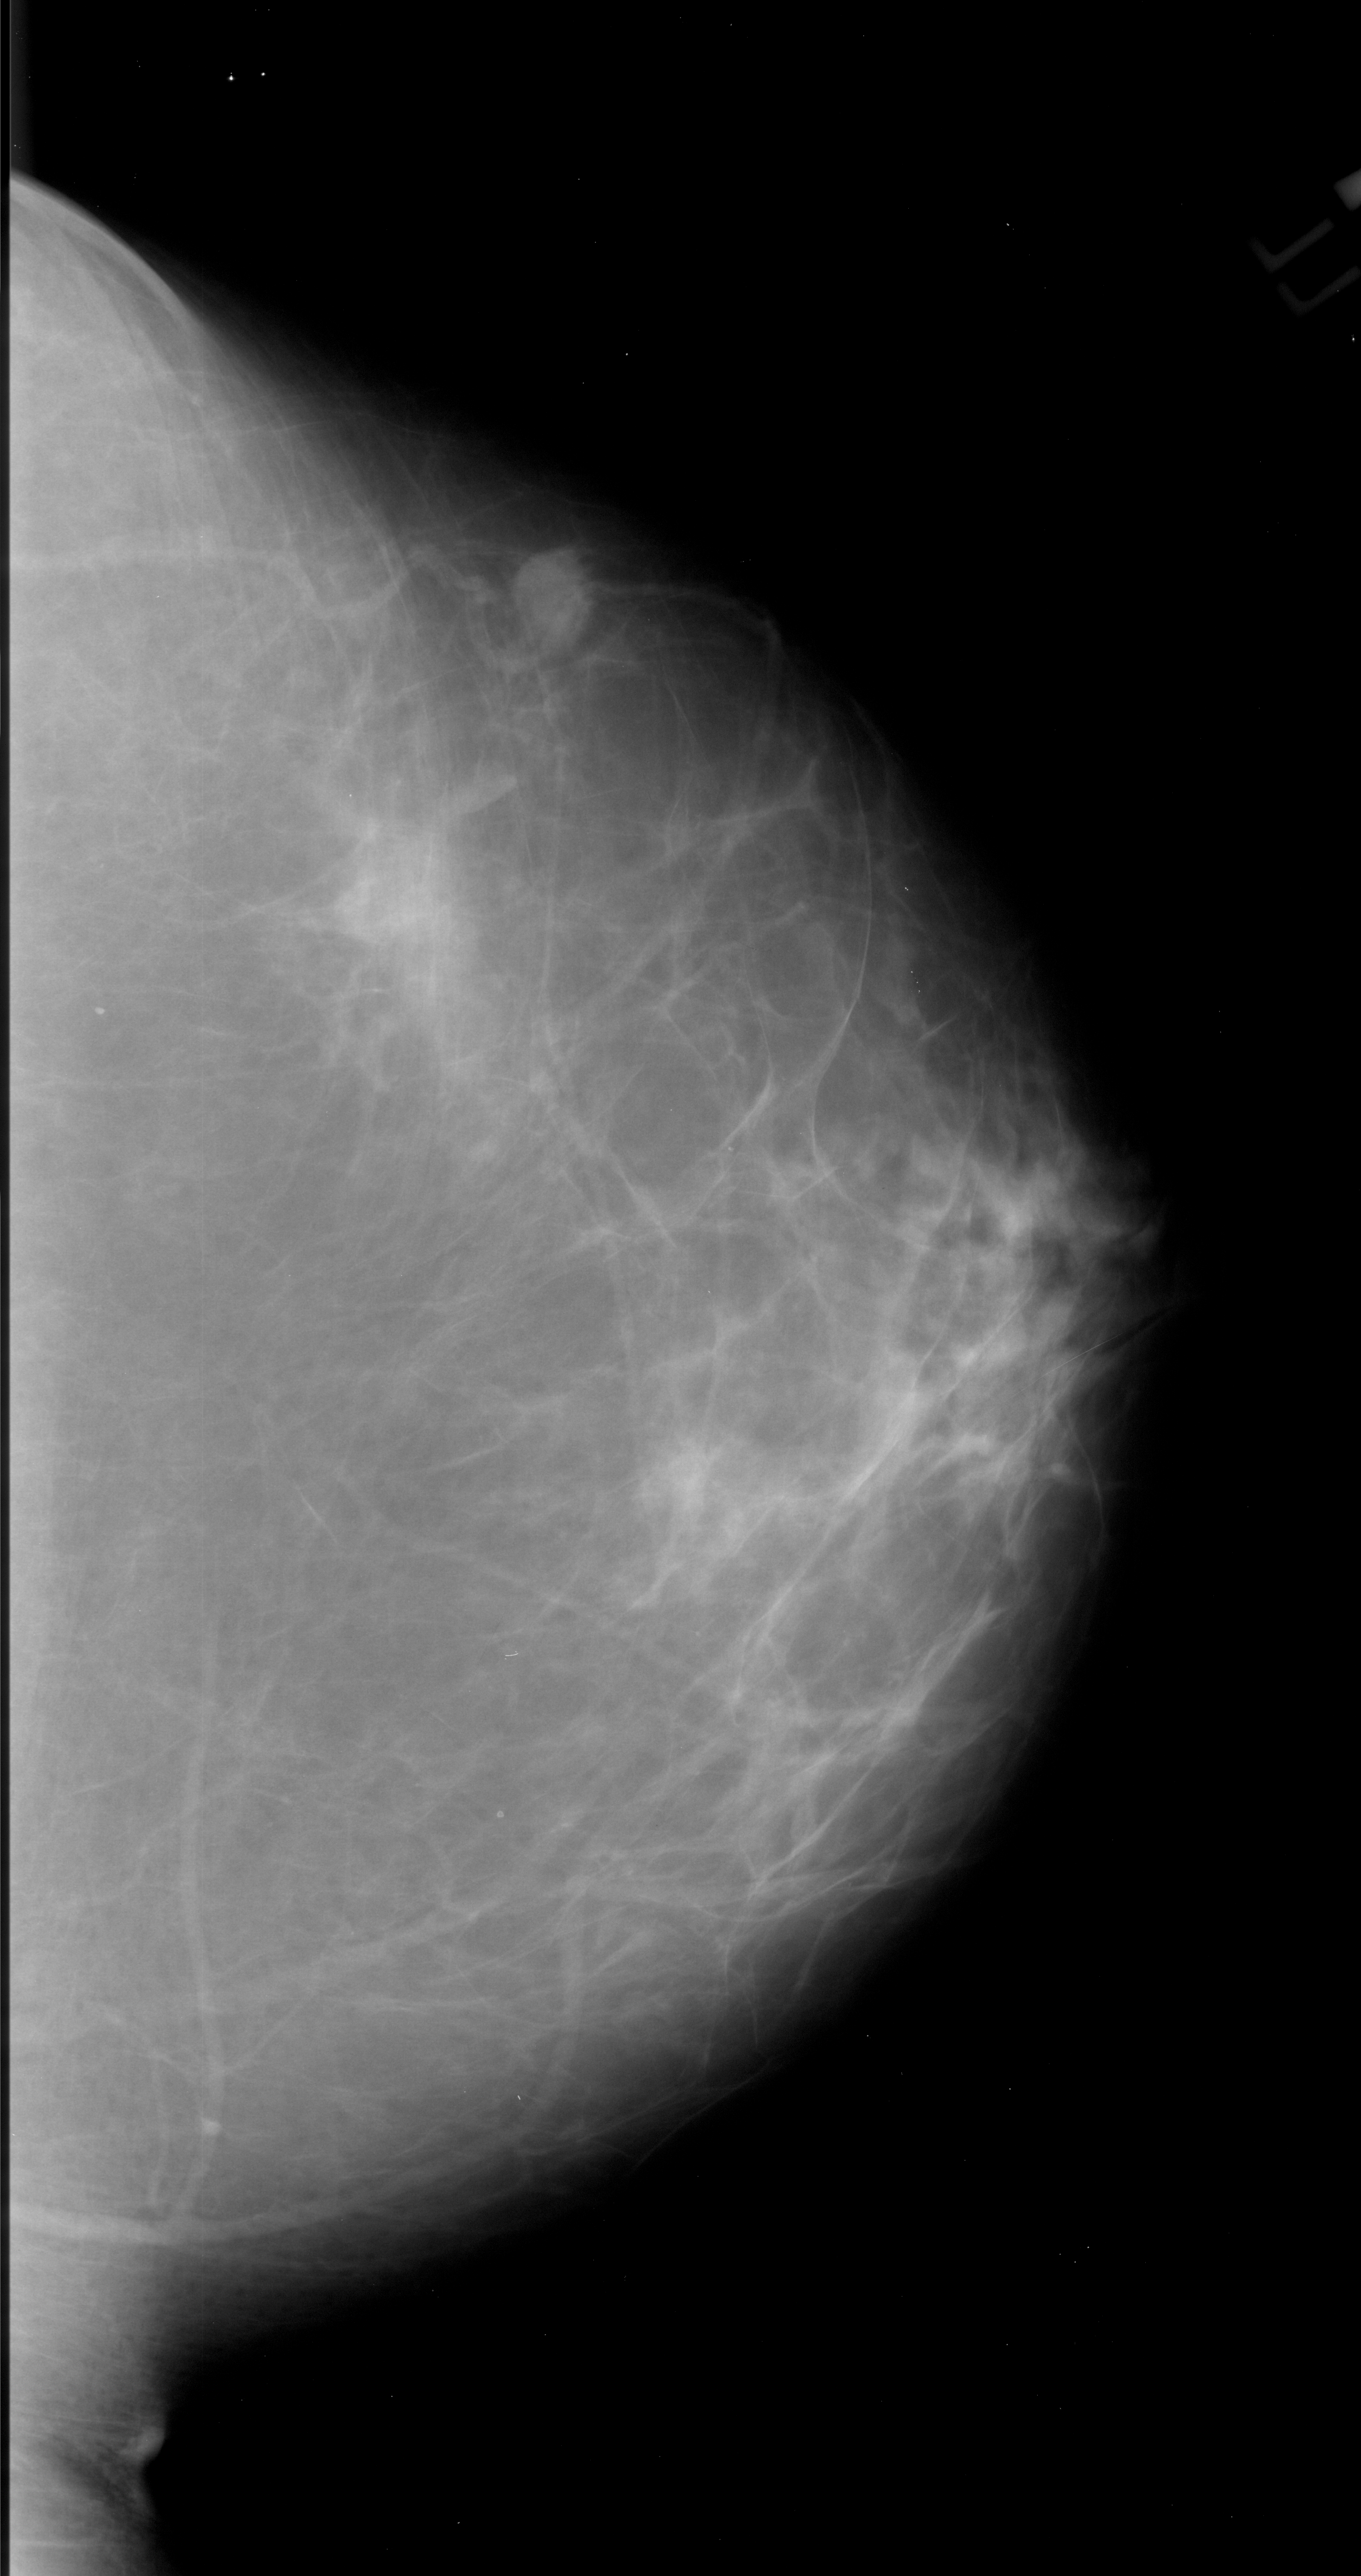
Mammogram (digitized film). Right breast. CC view. BI-RADS breast density category 2 (scale 1–4). 1361 × 2576 image matrix.
Expert-marked regions of interest on this film, with their recorded descriptors:
- mass, shape round, margins ill defined; BI-RADS assessment category 4; subtlety rating 4 on a 1 (subtle) to 5 (obvious) scale; pathology (as recorded): malignant: bounding box <511,546,604,649> (left, top, right, bottom; pixels)